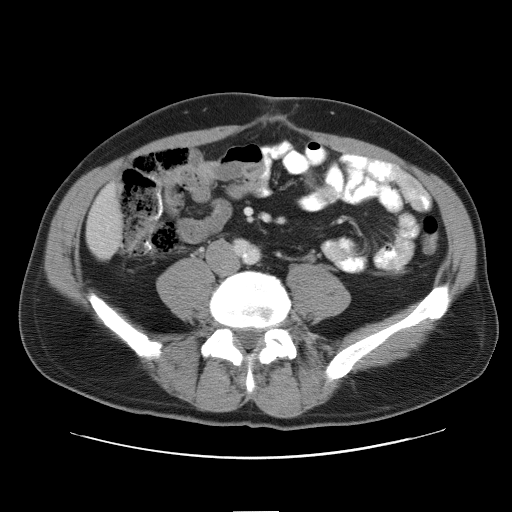
Contrast-enhanced abdominal CT, one axial slice. Position 10 of 52 along the scan axis. Reconstruction kernel STANDARD. Intravenous contrast given. Soft-tissue window (W 400 / L 40 HU). 512 × 512 image matrix, field of view 393 × 393 mm. Male patient, age 70 years. From the clinical record (not read from this slice): diagnosis: colorectal cancer liver metastases, imaged before liver resection; multiple liver metastases: yes; largest metastasis: 4 cm; disease in both lobes: yes.
Annotated regions visible in this slice (expert manual segmentation):
- liver: box from (x=88, y=187) to (x=123, y=260) px